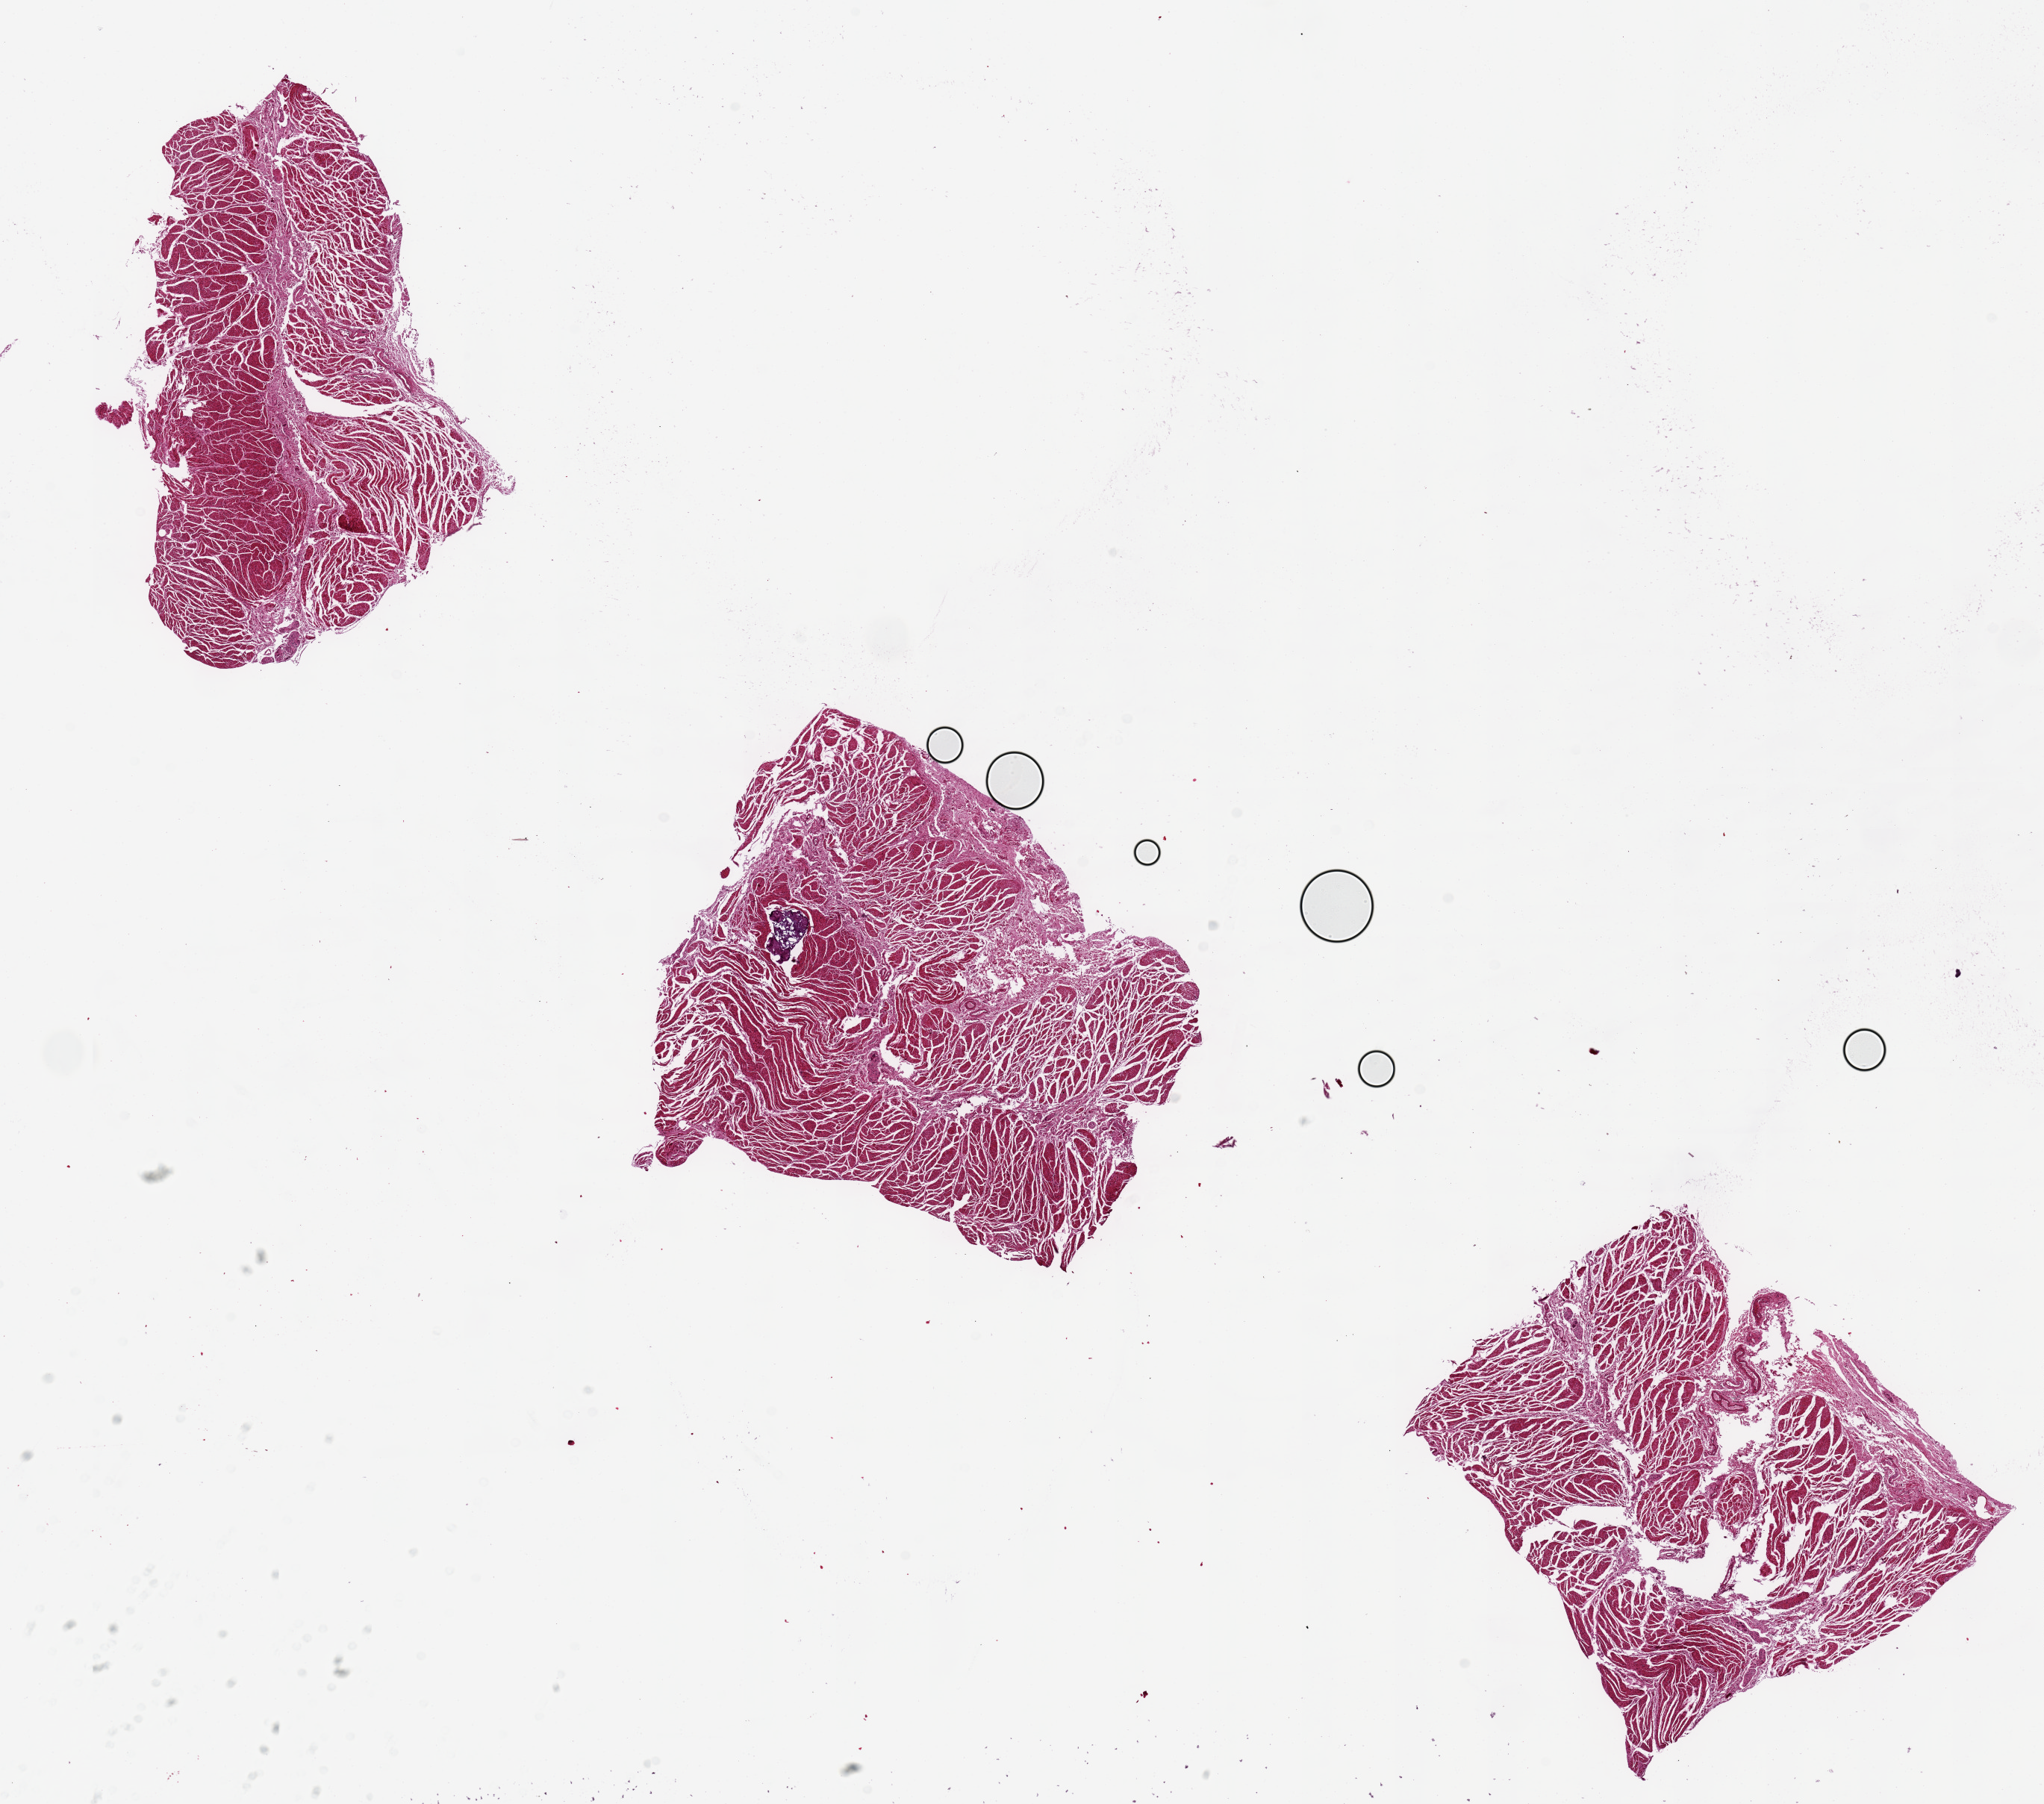
Digitized H&E-stained section — a low-resolution overview of the entire scanned area, about 21.7 x 19.1 mm (slide scanned at 20x); PAXgene-fixed, paraffin-embedded tissue; sampled site (target tissue): esophageal muscle; tissue donor sample. Donor: female.
Reviewer comment on this tissue sample: mild edema.